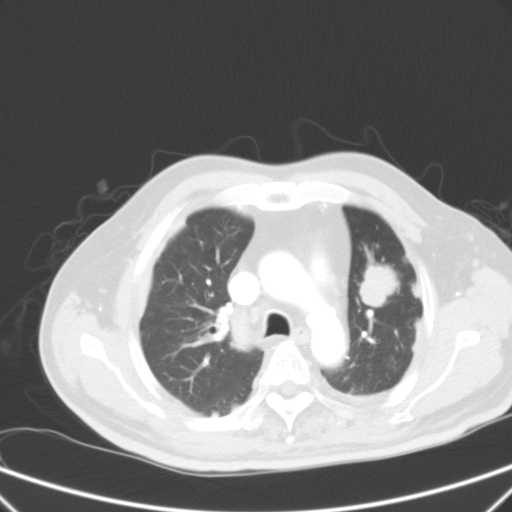
Chest CT, one axial slice. Slice 42 of 59 in the series (ordered by position). 120 kVp. Intravenous contrast given. Lung window (W 1500 / L -600 HU). 5 mm slice thickness. 512 × 512 image matrix, field of view 357 × 357 mm. Patient: male, 66 years. From the clinical record (not read from this slice): clinical TNM (as recorded): T1c N3 M1a.
Annotated regions visible in this slice (bounding box drawn by a radiologist):
- lung tumour (recorded histology: squamous cell carcinoma): bounding box [x1, y1, x2, y2] px = [354, 258, 404, 315]